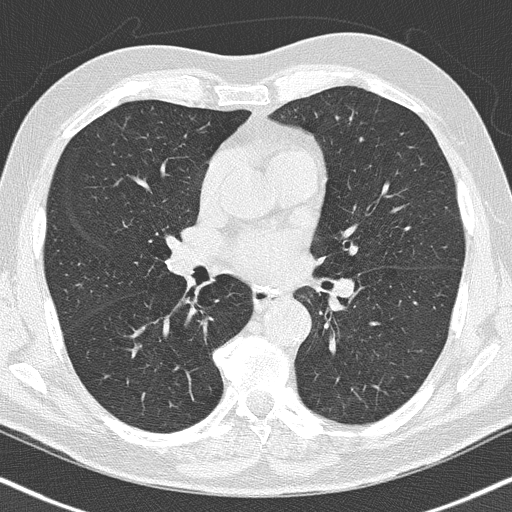
Axial slice from a low-dose chest CT screening exam; first (baseline) screen; lung window (W 1500 / L -600 HU); 2 mm slice thickness; 120 kVp; slice 88 of 186 in the series; 512 × 512 image matrix, field of view 324 × 324 mm. Male, age 66 years at enrolment.
• Expert-annotated lung lesion, bounding box <185,271,208,297> (left, top, right, bottom; pixels).
• The exam's reader record, not a measurement of the box and not confirmed to be the same lesion: non-calcified nodule or mass ≥4 mm, right upper lobe, 5 × 4 mm, smooth margins.
• Later outcome: lung cancer diagnosed 778 days after this screen — squamous cell carcinoma, NOS, right lower lobe, poorly differentiated (G3), stage IIA (AJCC 6th edition), 22 mm at pathology.